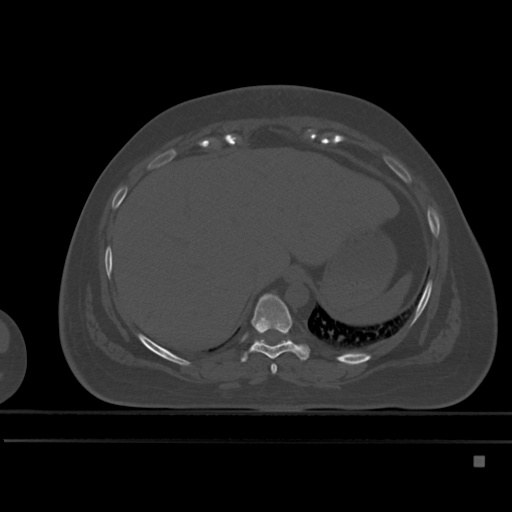
CT including the spine, one axial slice. Position 261 of 495 along the scan axis. Bone window (W 1800 / L 400 HU). 1.5 mm slice thickness. 512 × 512 image matrix, field of view 404 × 404 mm. Female patient, age 33 years. From the clinical record (not read from this slice): primary cancer: breast; vertebrae with lytic lesions (as recorded): T1.
Outlined on this slice (semi-automatic segmentation, software-assisted and operator-edited):
- T10 vertebra: bounding box [x1, y1, x2, y2] px = [253, 338, 292, 345]
- T8 vertebra: [271, 364, 277, 374]
- T9 vertebra: [241, 293, 310, 362]